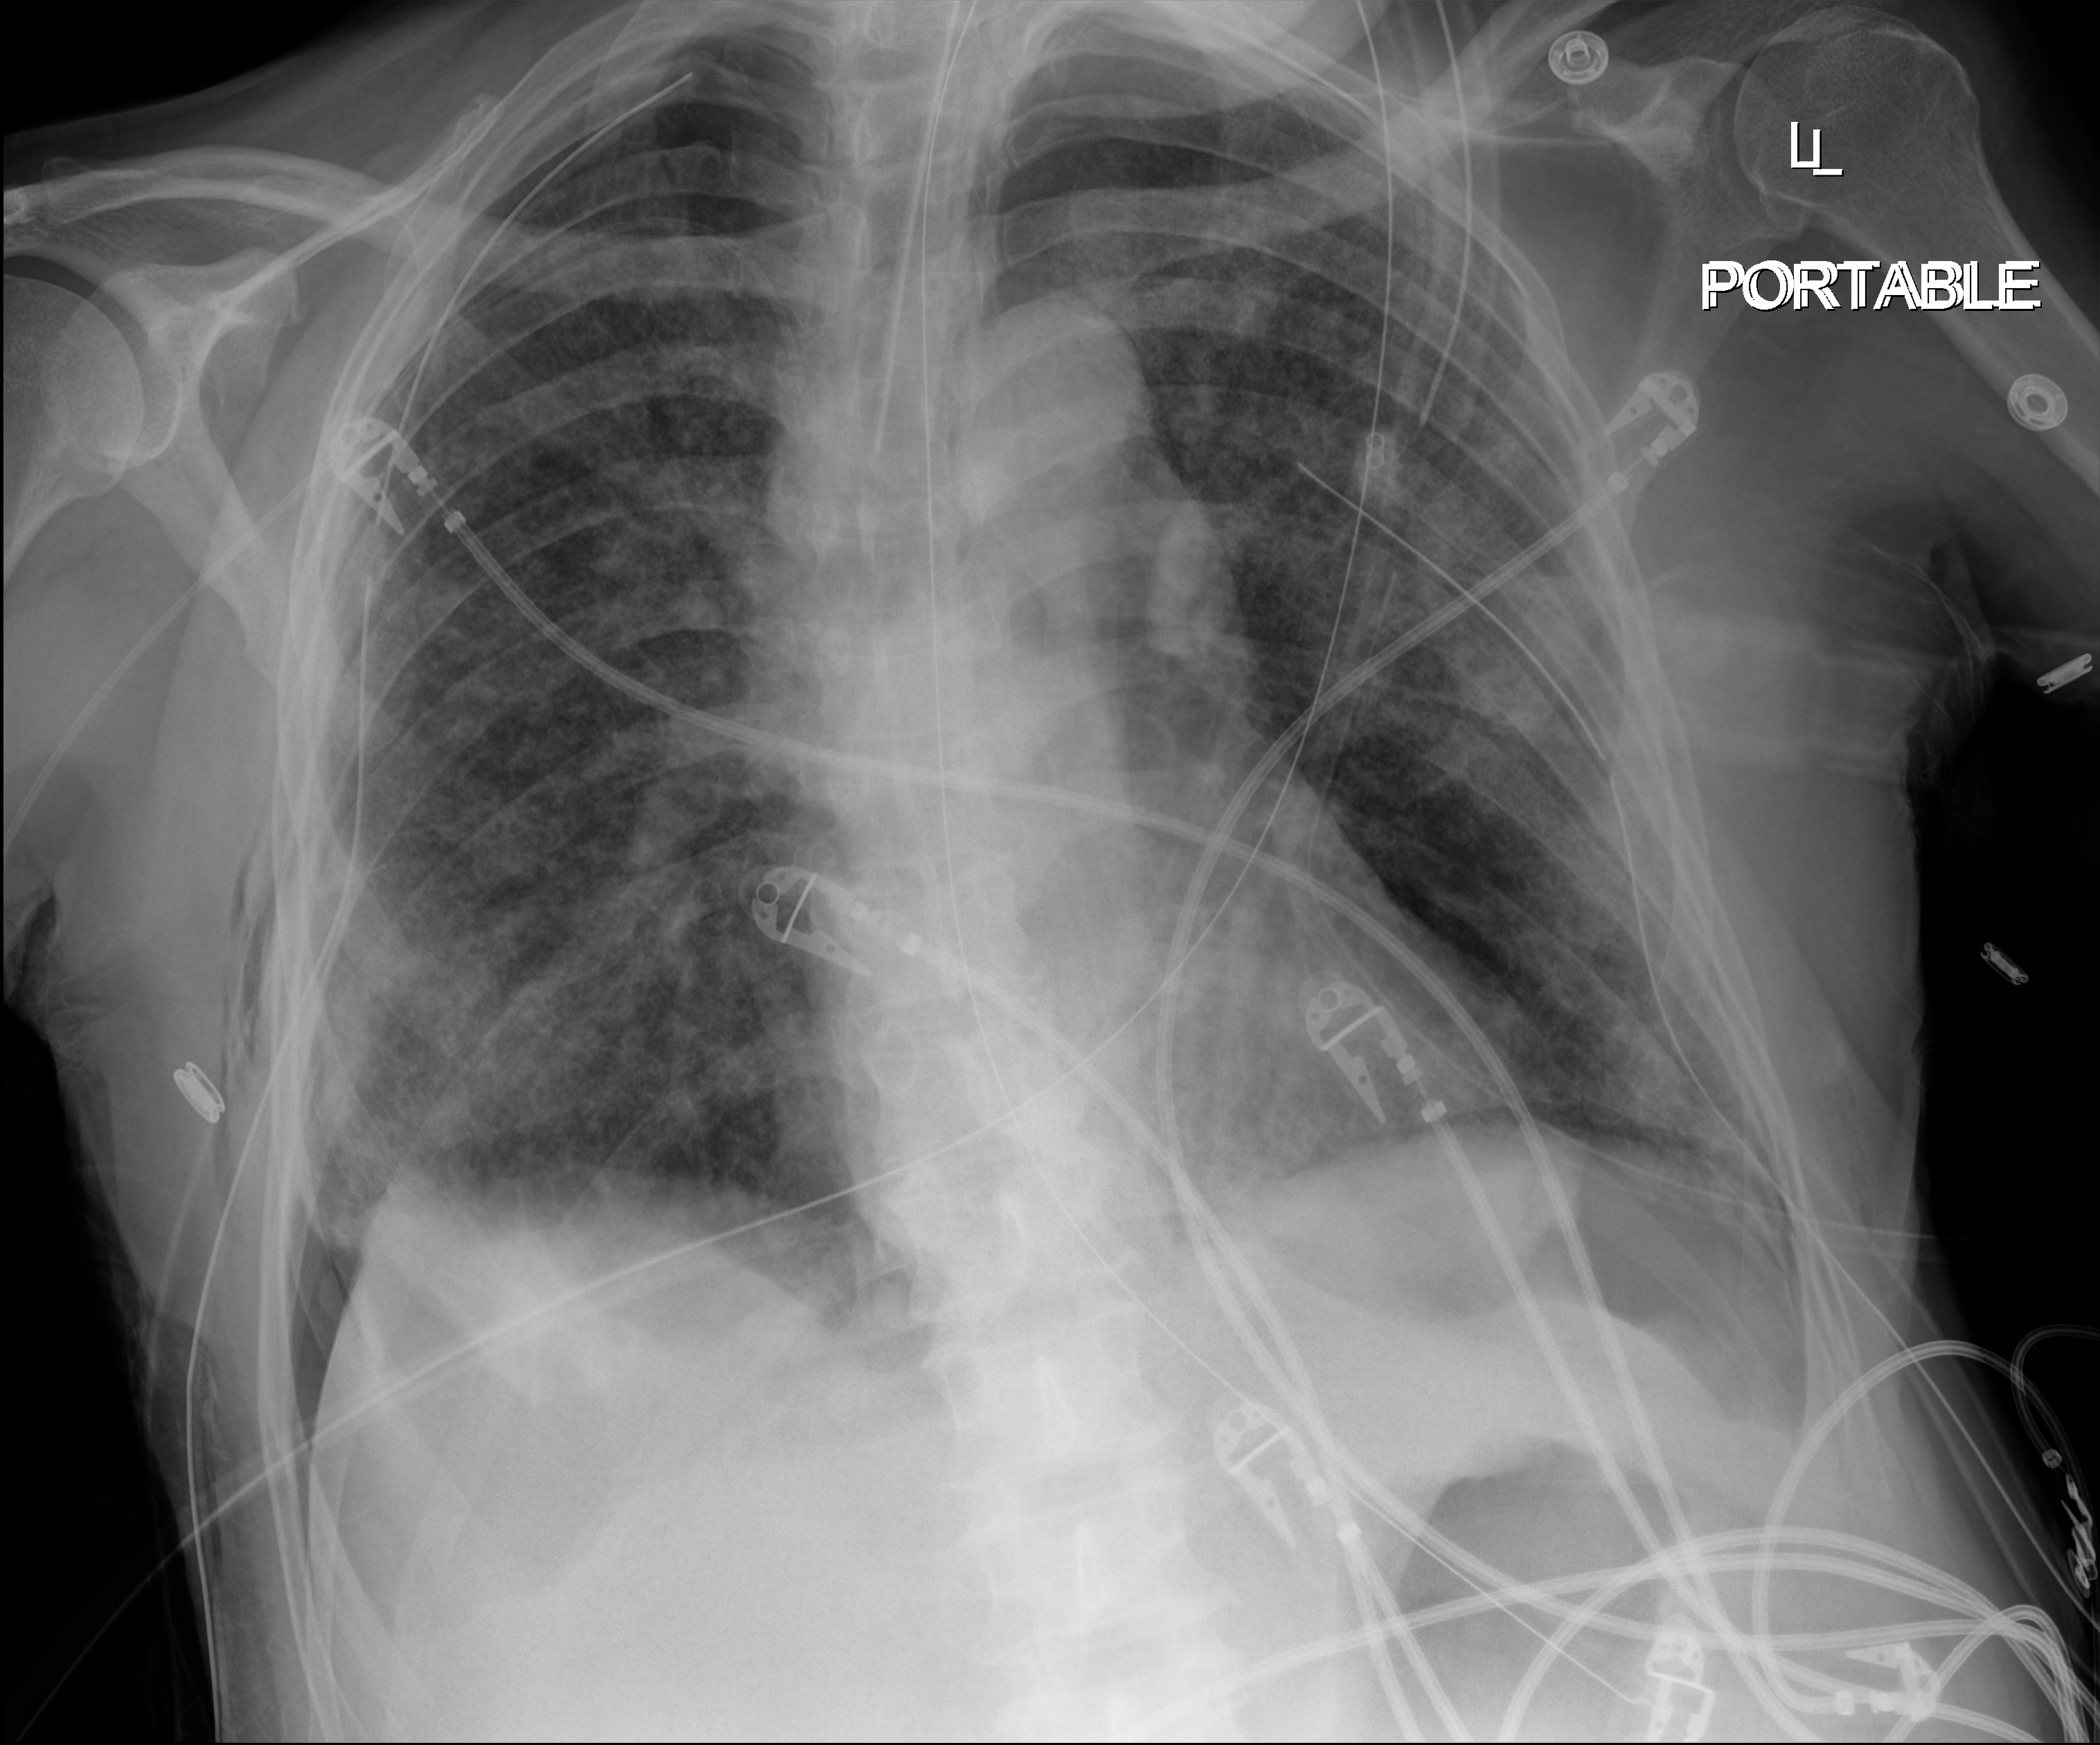
Portable chest radiograph; anteroposterior (AP) projection. Male patient hospitalised with COVID-19, age 60–74 years.
From the hospital-stay record, not from the radiograph (when in the stay this image was taken is not recorded): other chronic lung disease (admission record): yes.